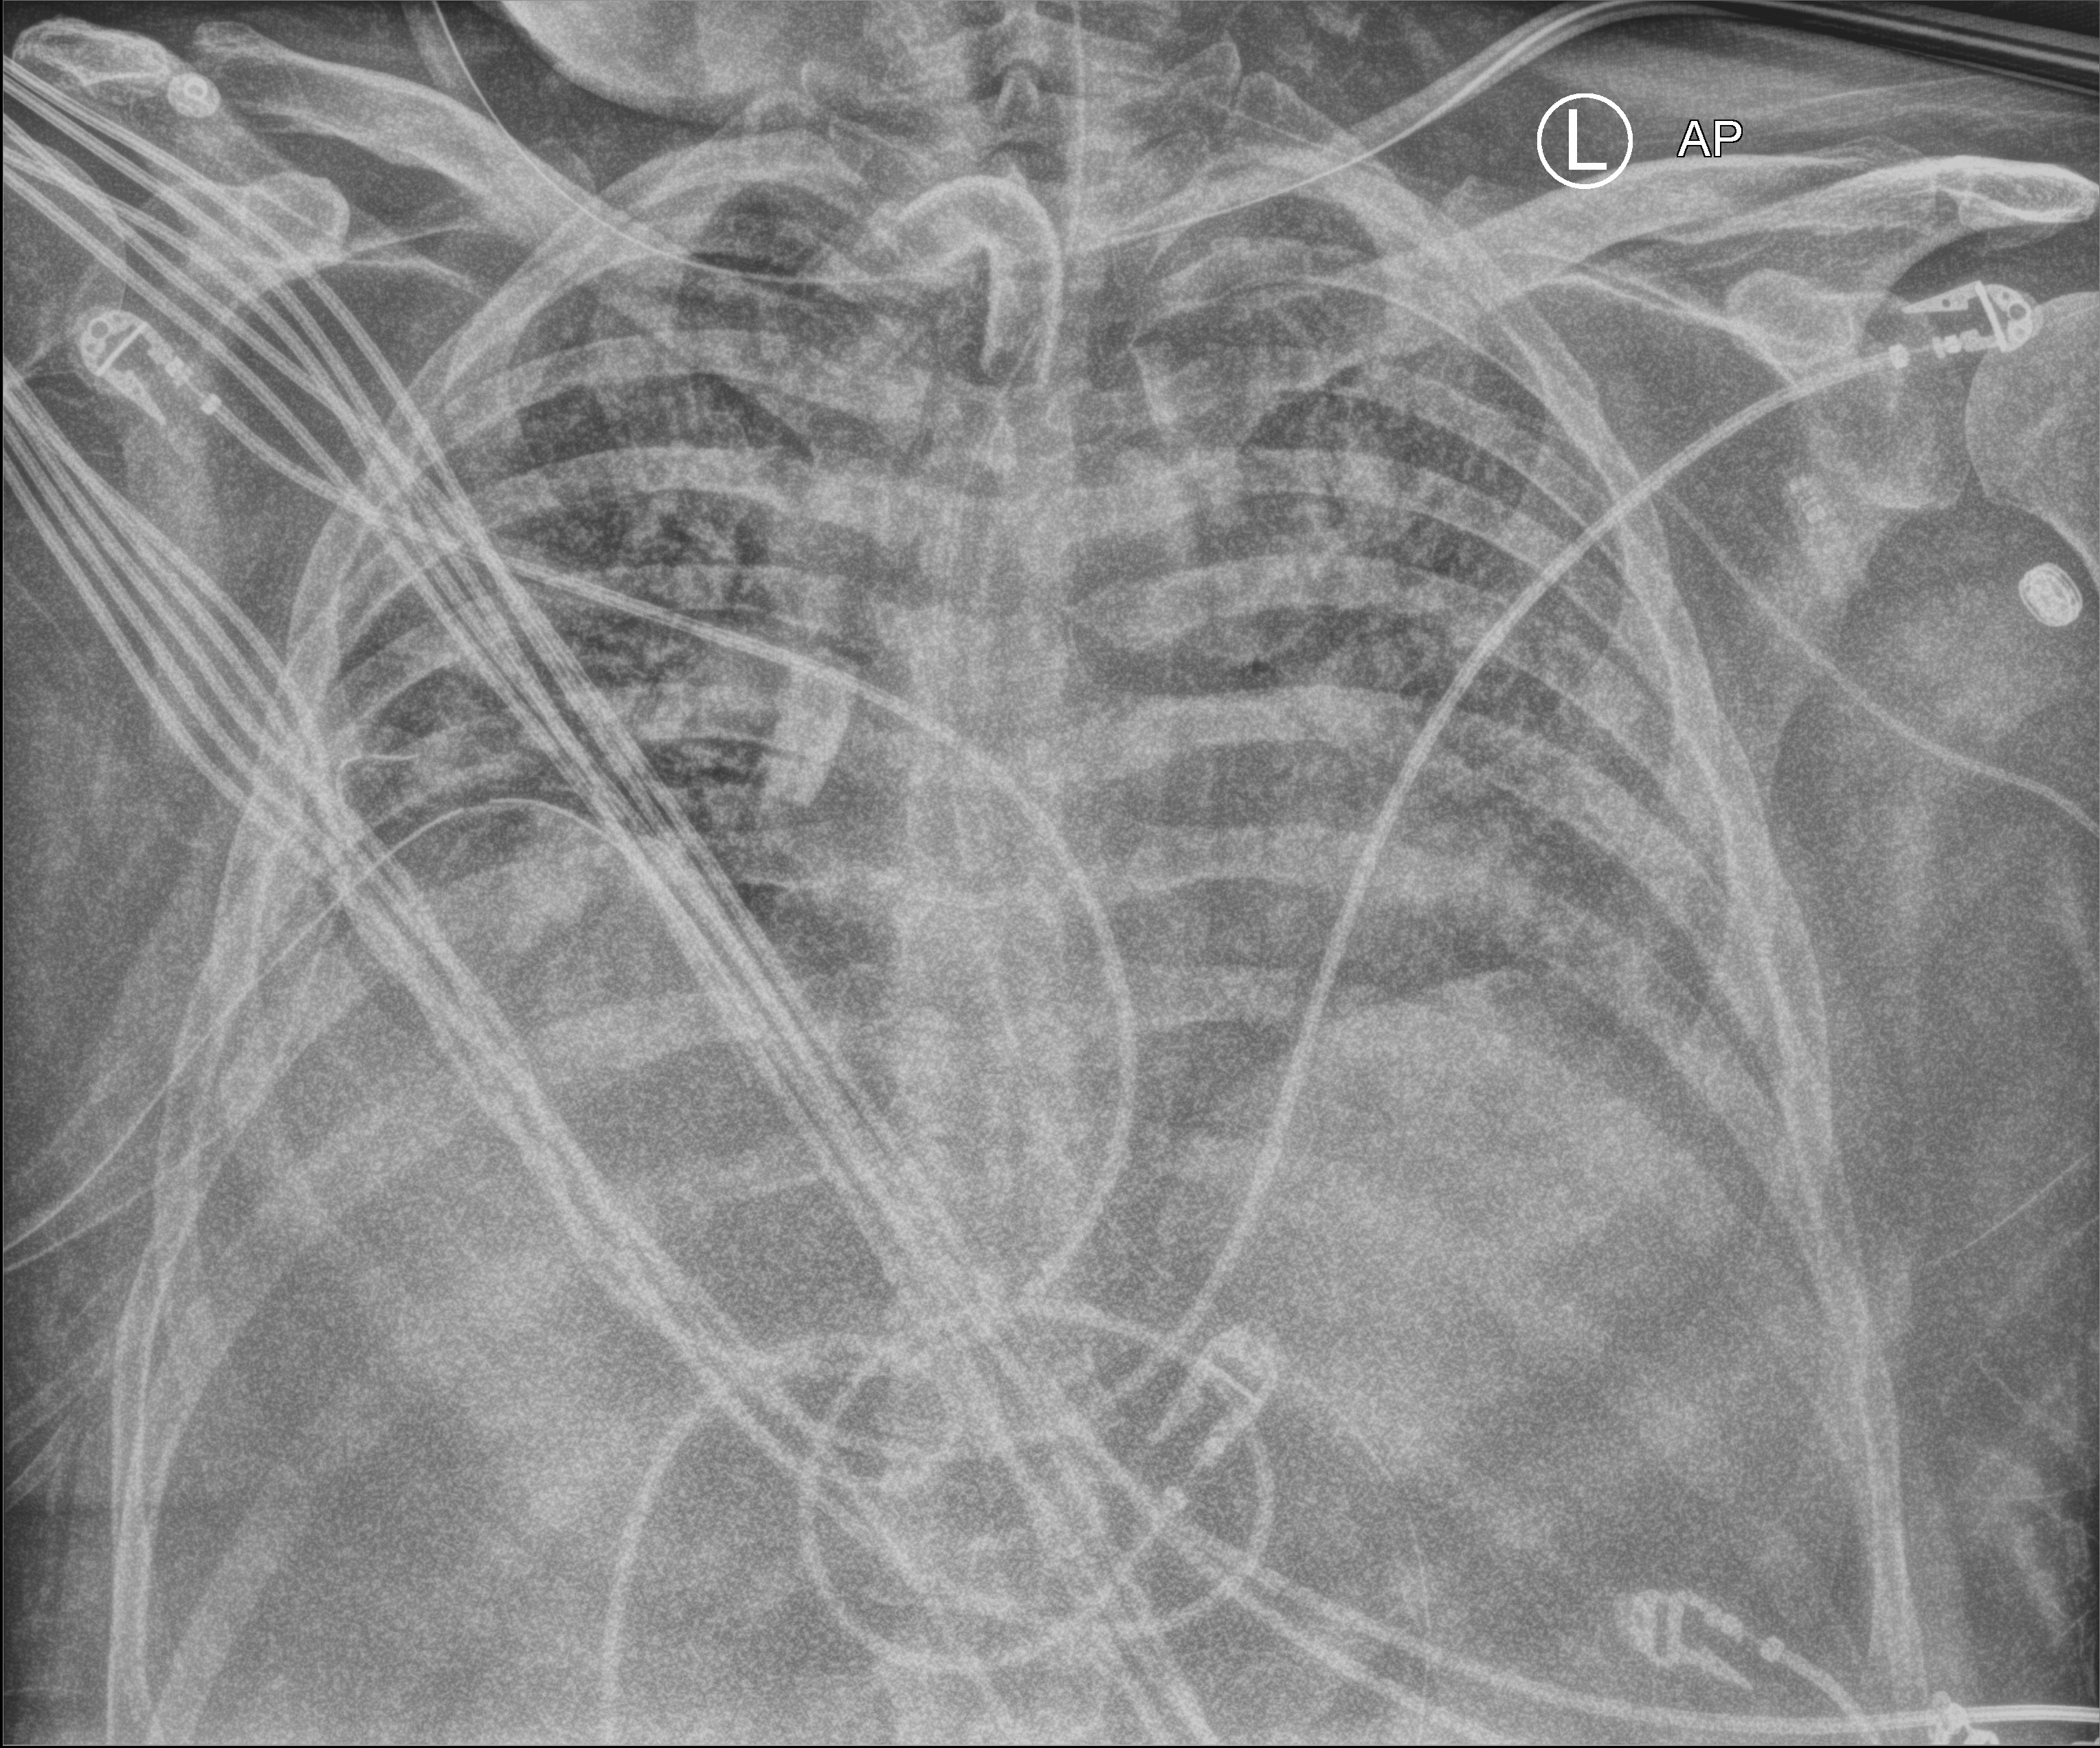
Chest X-ray (portable). Patient hospitalised with COVID-19; male, aged 18–59 years.
Admission-level facts for this patient (not findings on this image; timing relative to this image not recorded):
- admitted to intensive care during this hospital stay: yes